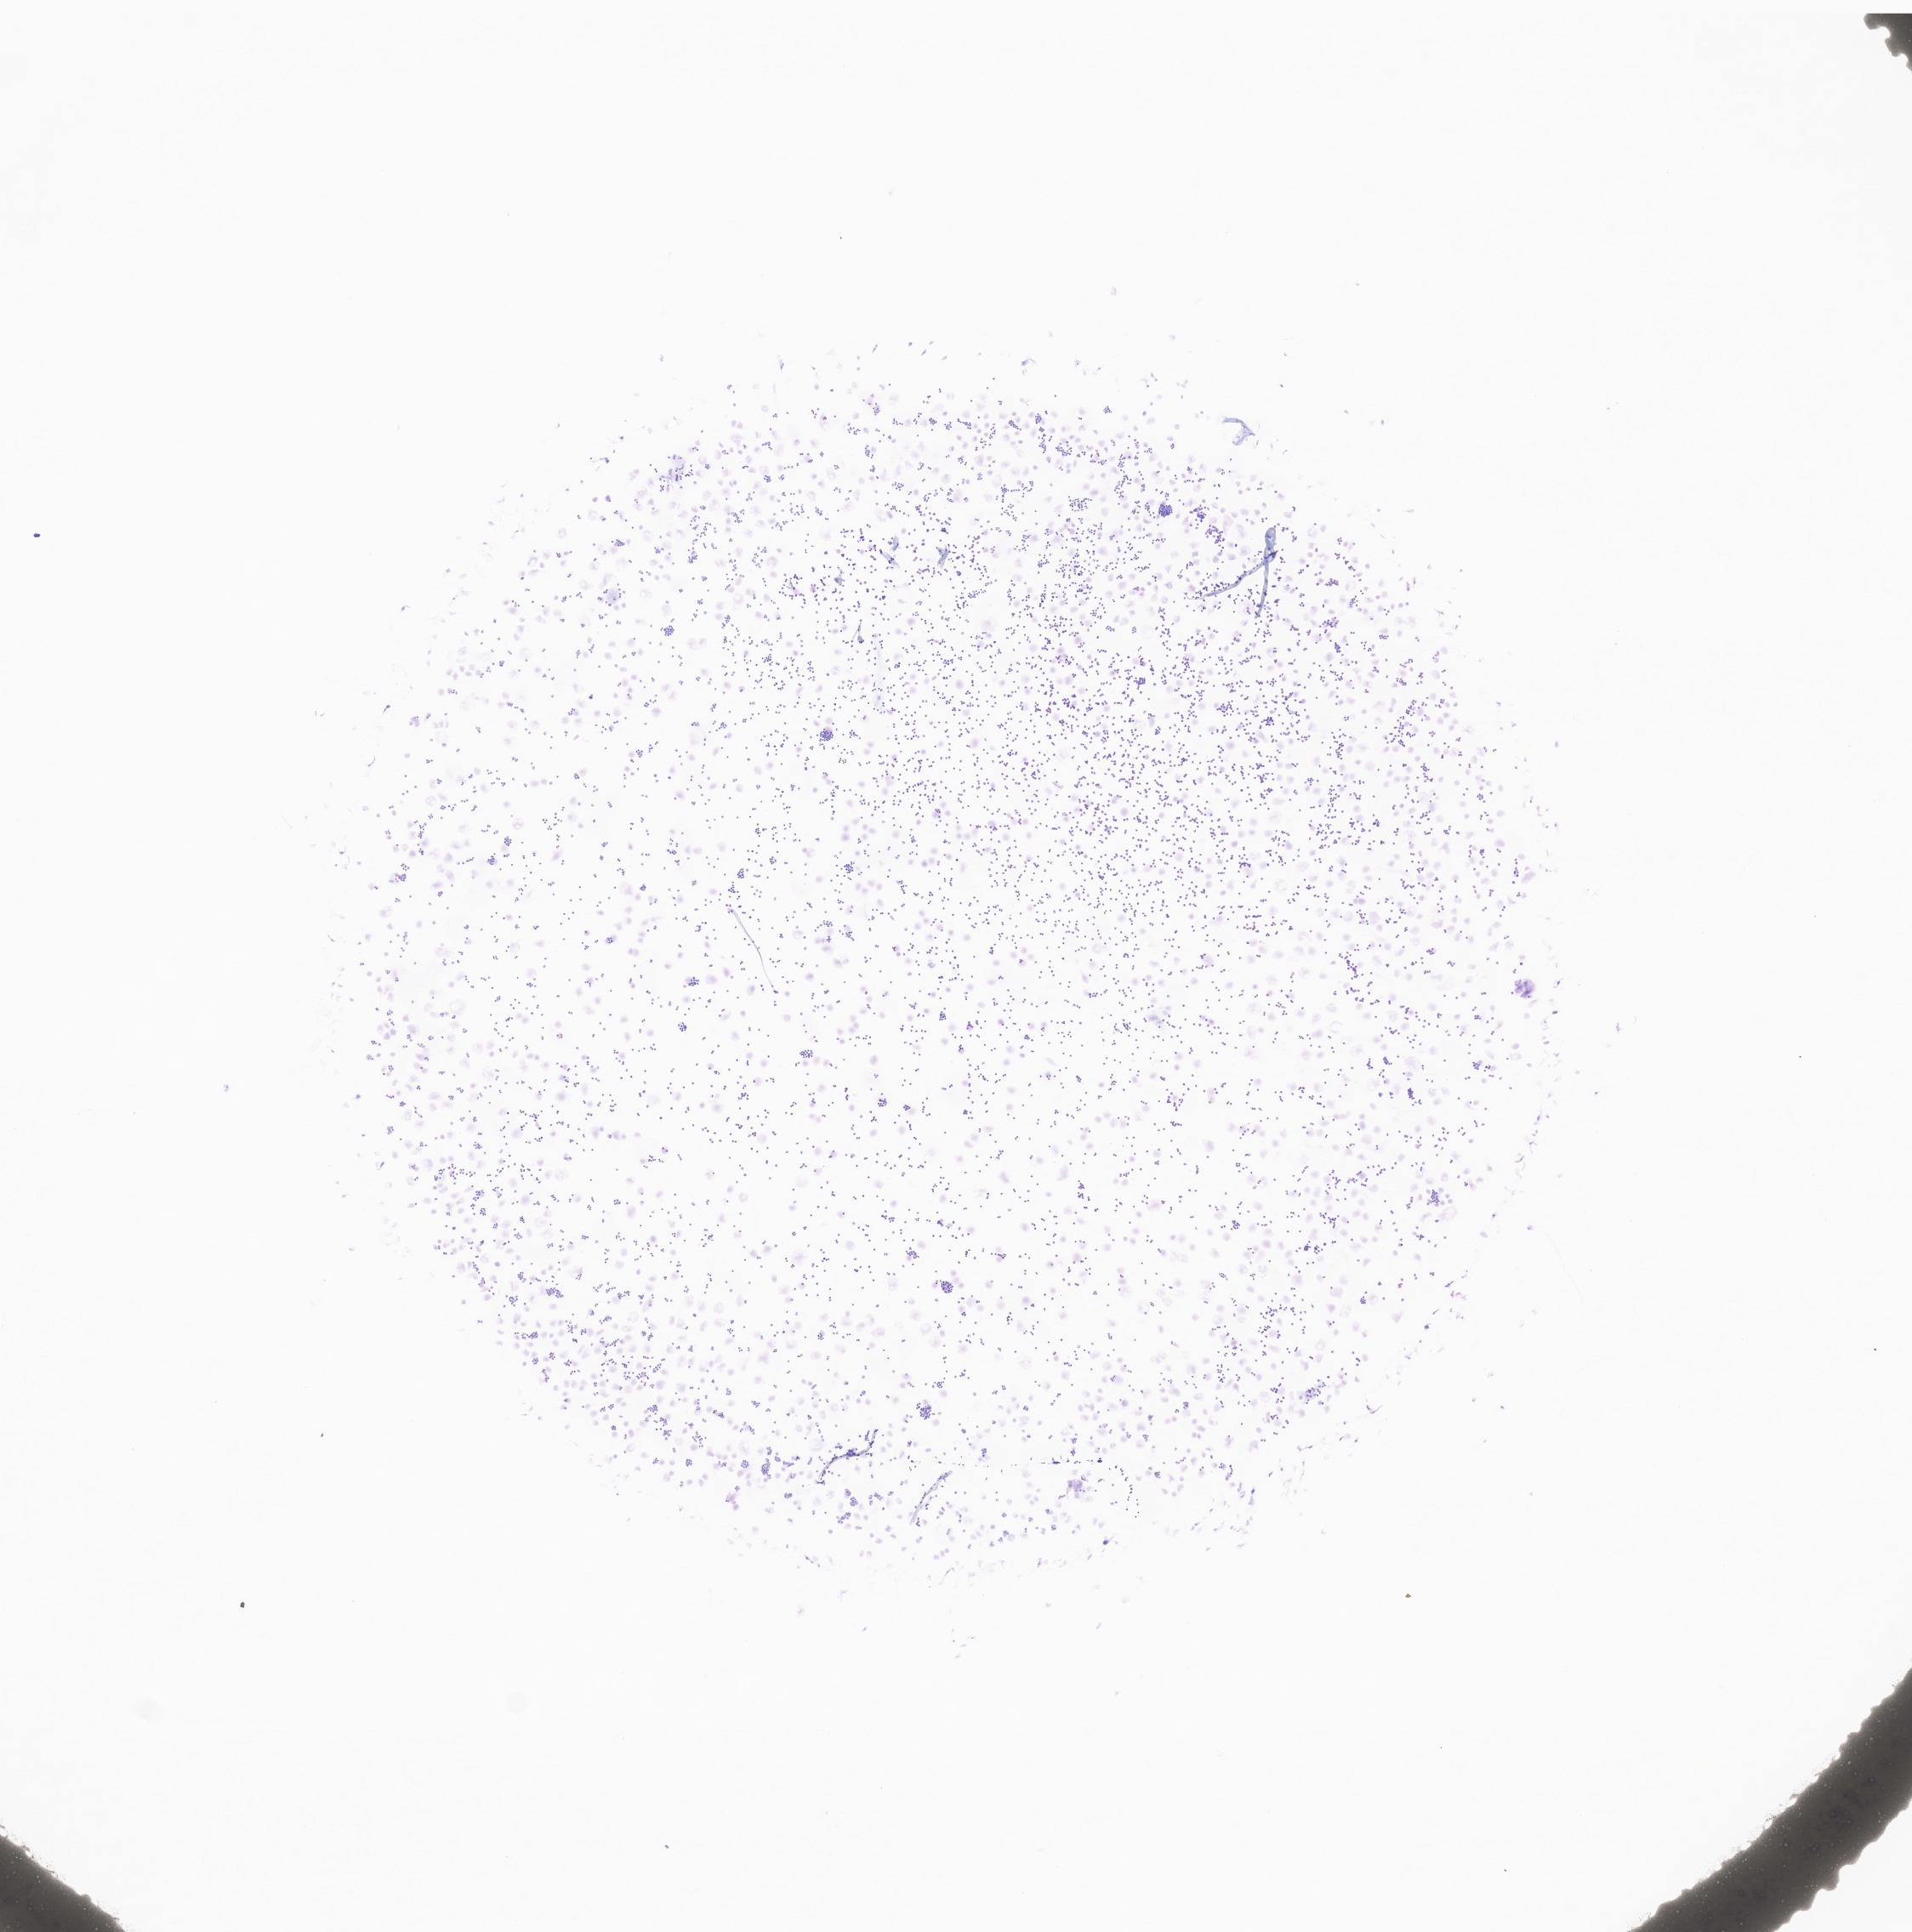
Whole-slide image of tumor tissue from the bone marrow — low-resolution overview of the scanned area, about 9.5 x 9.6 mm. Female patient, age 33 months (2 years 9 months).
Diagnosis (ICD-O-3 morphology term): Neuroblastoma, NOS.